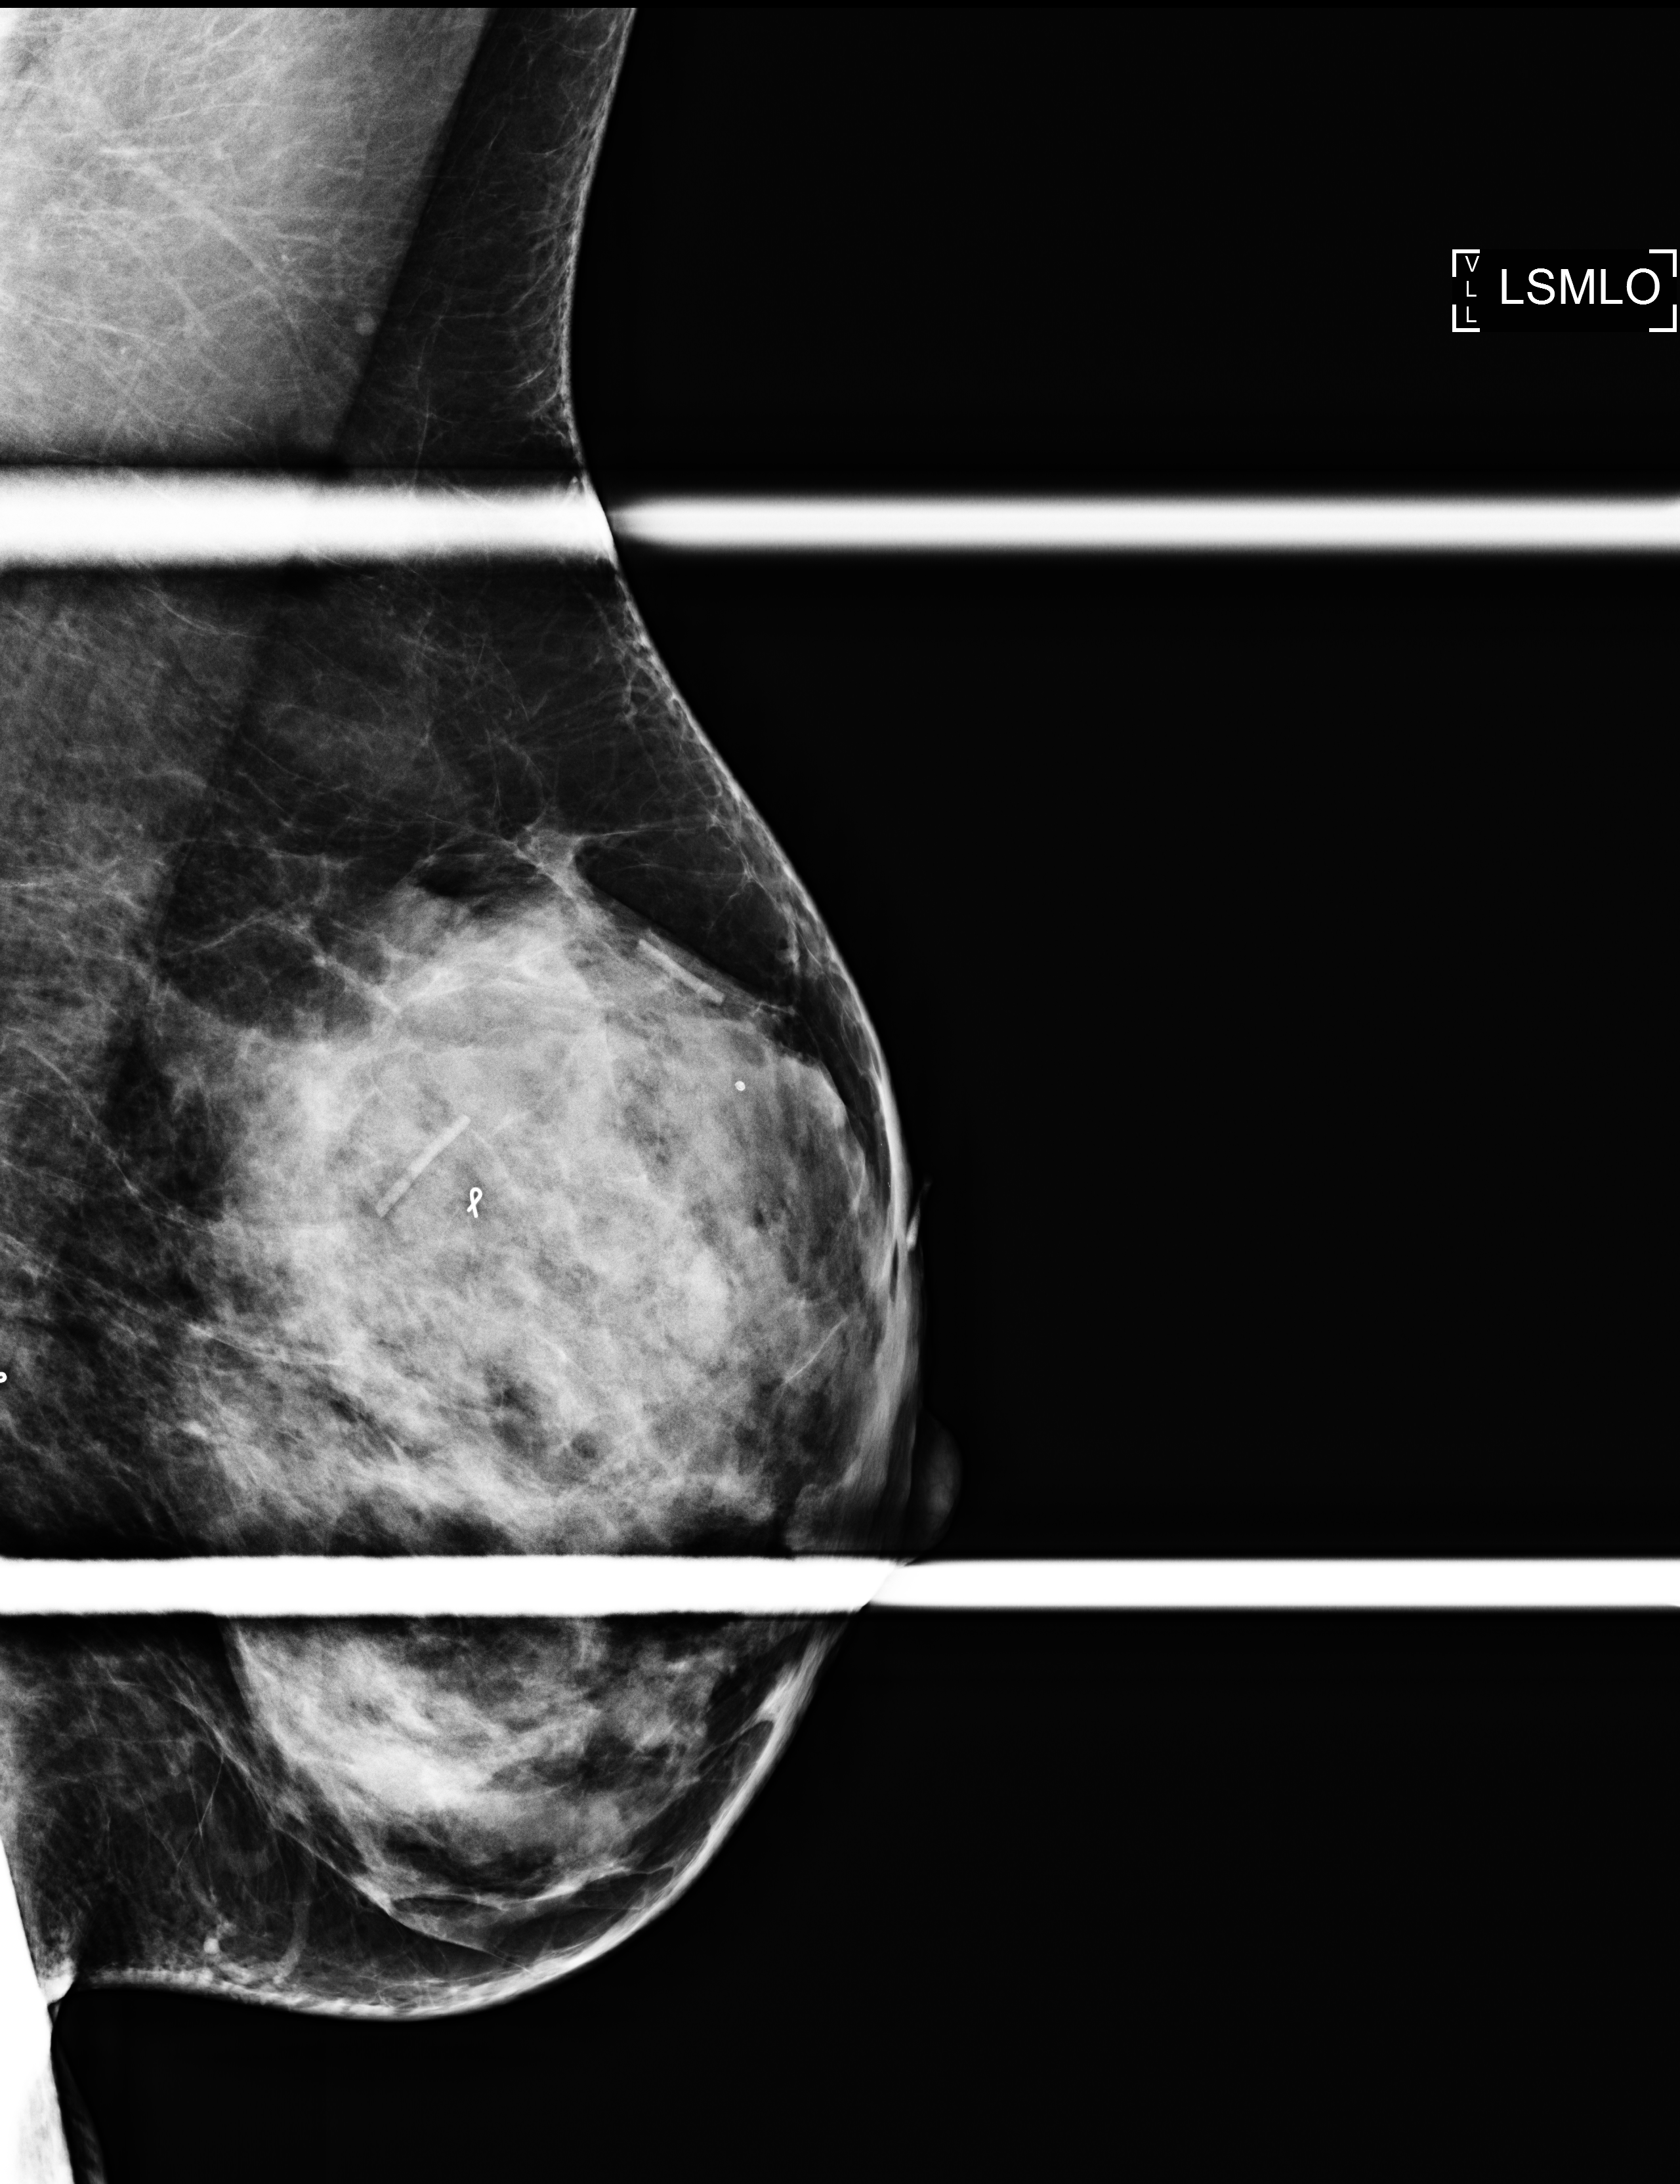
Additional work-up view. Female patient, age 48 years.
Image type: full-field digital mammogram. Breast: left. Projection: MLO view, spot compression.